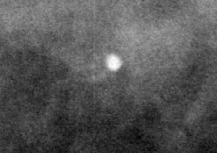
Crop from a digitized film mammogram around one marked abnormality; left breast; CC view; BI-RADS breast density category 3 (scale 1–4).
- Calcifications, morphology round and regular / lucent center; BI-RADS assessment category 2; benign; no additional work-up was recommended (benign without callback).